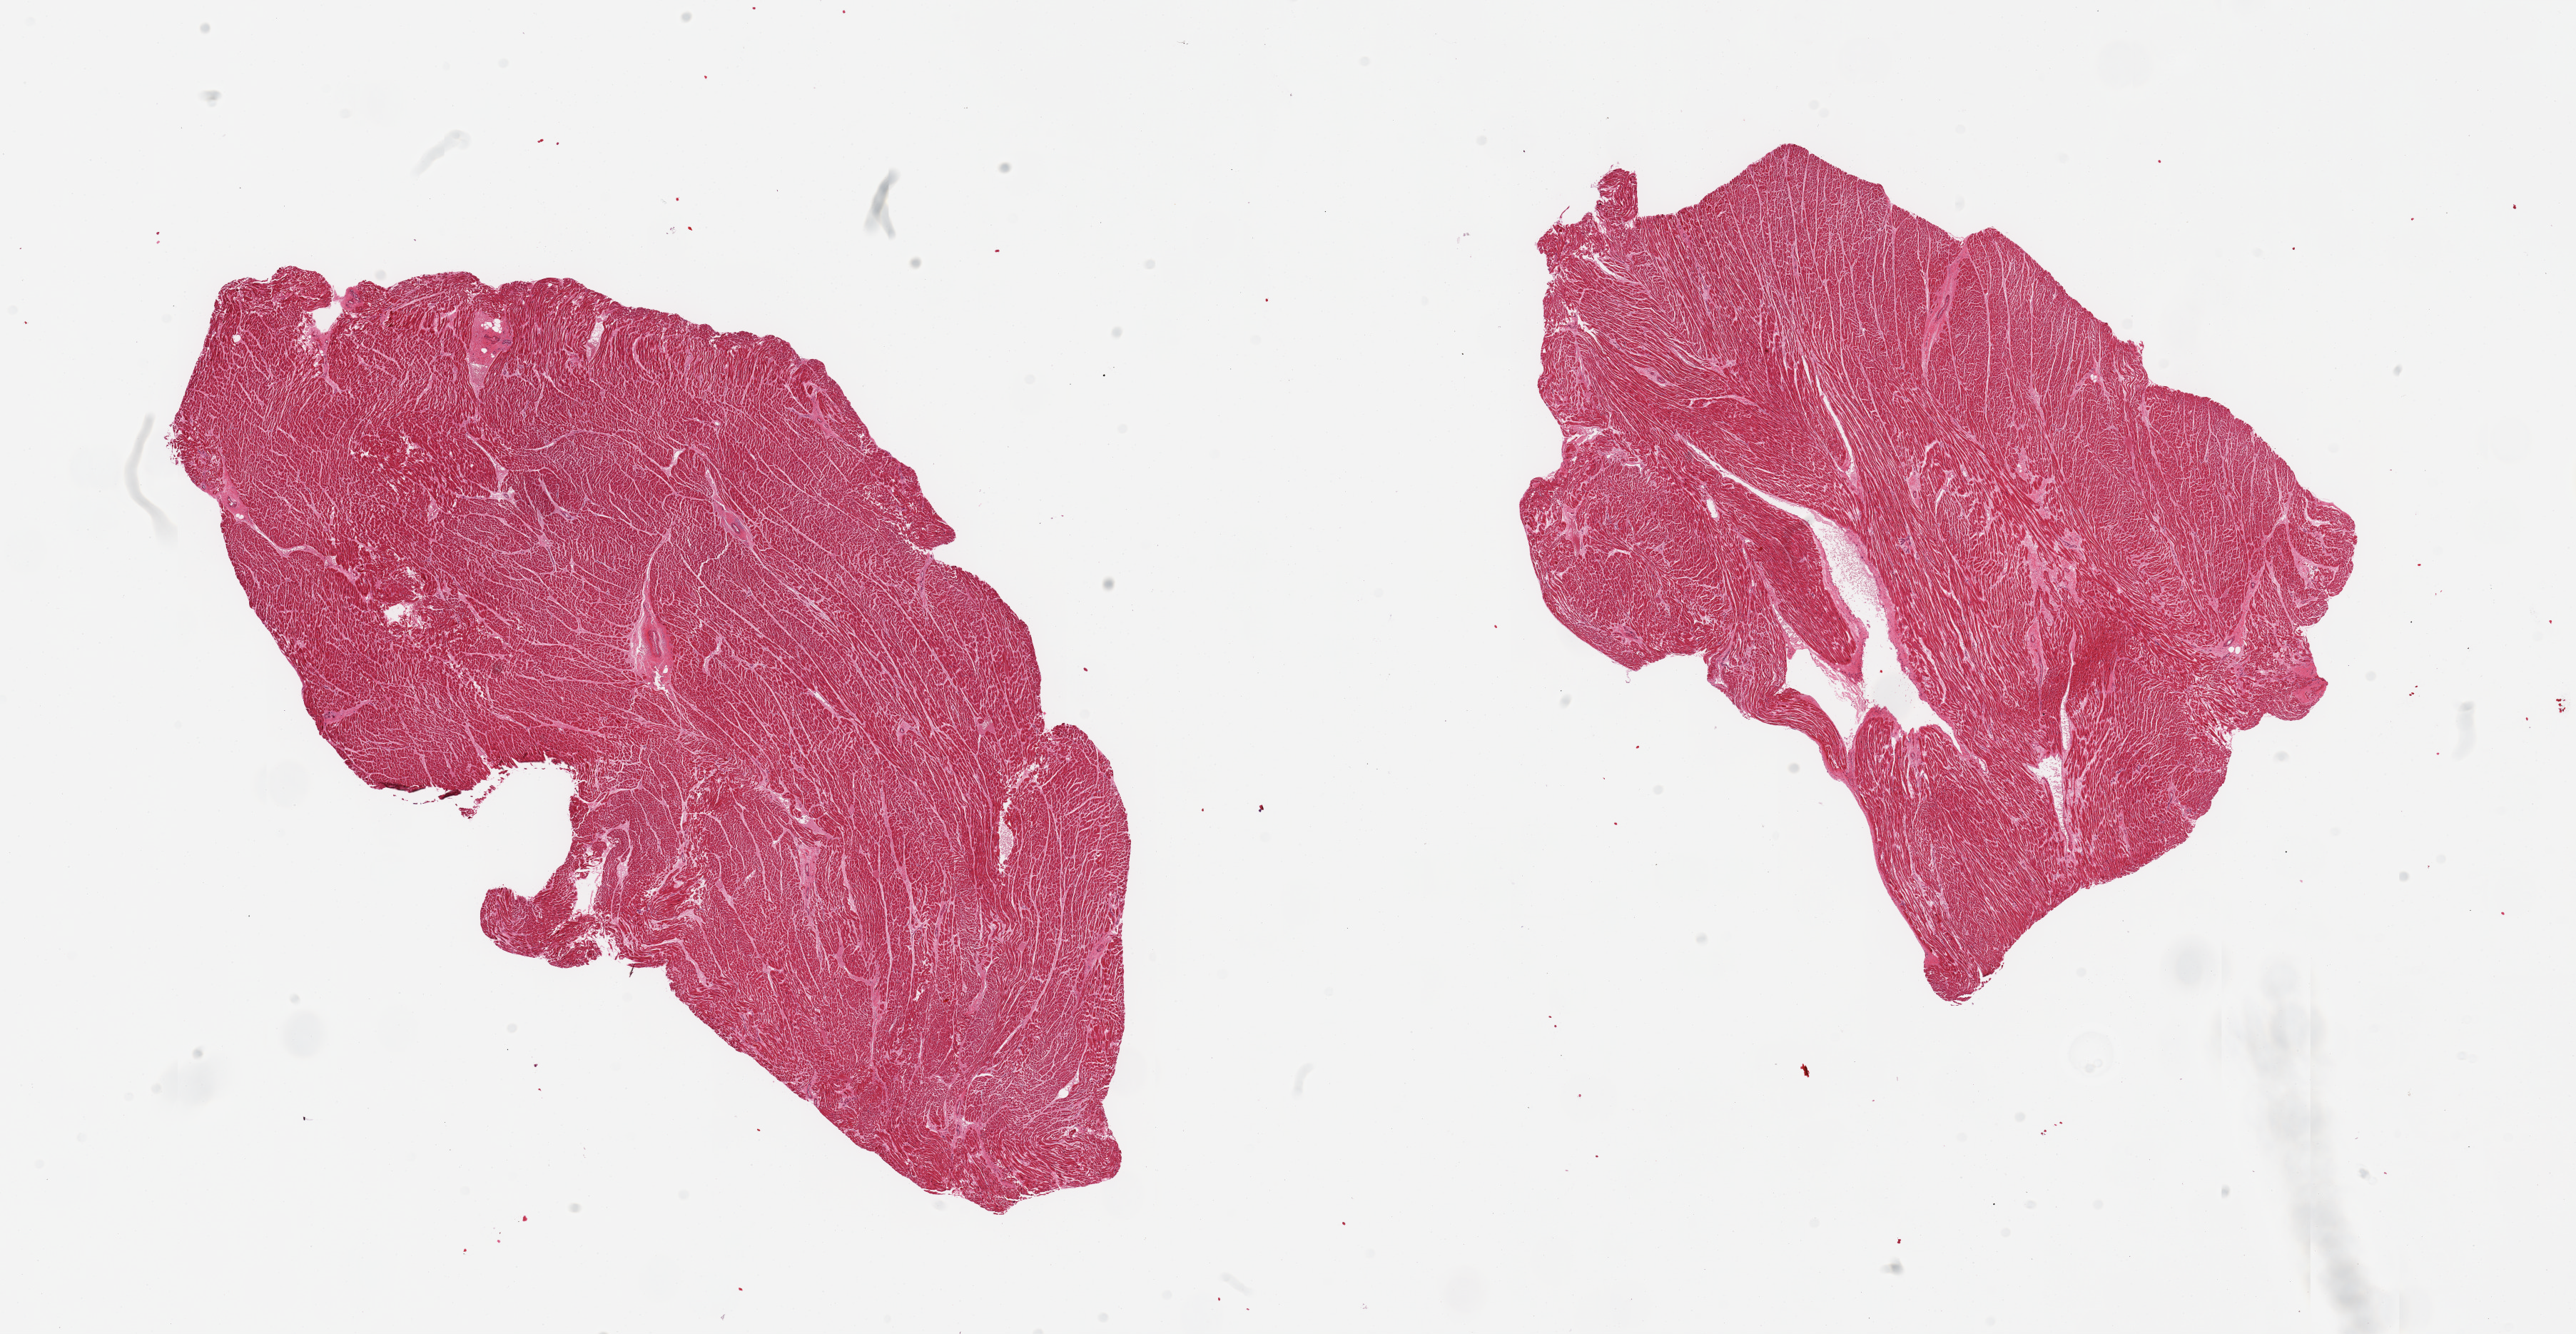
Haematoxylin and eosin whole-slide image, shown as a low-resolution overview of the whole scanned area (about 28.5 x 14.8 mm), PAXgene-fixed paraffin-embedded (PFPE) section, sampled site (target tissue): heart, donor tissue sample. Donor: male.
Pathologist's review note for this sample: 2 pieces.